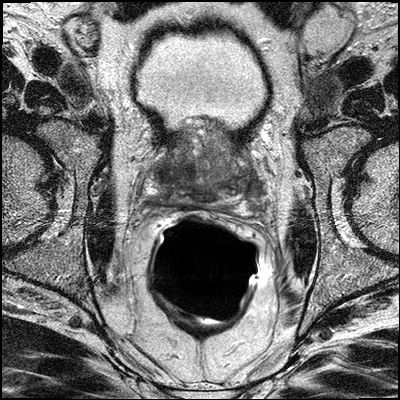
Multiparametric prostate MRI examination; 3 images, each a single mid-volume slice chosen by position (not for content). Treatment context recorded for this patient: Surgery.
Image 1: axial T2-weighted image, slice 19 of 36, 3 mm slice thickness.
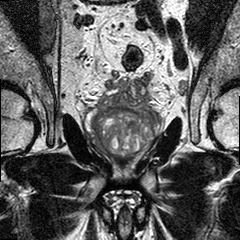
Image 2: T2-weighted coronal slice, series "T2W_TSE_COR", slice 14 of 26.
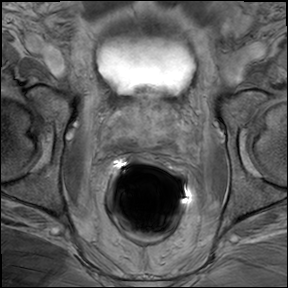
Image 3: DCE (dynamic gadolinium-enhanced) axial slice, slice 18 of 34, dynamic phase 5 of 8, 6 mm slice thickness.
Report of this MRI examination:
FINDINGS: The zonal anatomy is preserved. Due to BPH with prominent middle lobe of the prostate is enlarged measuring 5 x 4 x 5 cm resulting in an estimated volume of 52 cc There is diffuse signal alteration seen throughout the central gland consistent with BPH. There is a prominent middle lobe; There is also diffuse linear centrifugal signal alteration seen in the peripheral zones, due to chronic prostatitis, which might obscure small cancer foci. There are several sub 5 mm foci of suspicious enhancement seen in the left and right peripheral zones the prostate in all three levels (from base to apical third) . There is no suspicious enhancement of prostate capsule seen. There is no evidence of neural vascular bundle involvement. The folds of the seminal vesicles are thickened possible as consequences of longstanding BPH . Seminal vesicles infiltration therefore cannot be not entirely excluded, however no intraluminal masses seen in the seminal vesicles. Two rounded lymph node seen (12 x 8 and 9 x 11 mm respectively) along the iliac vessels on the right, just at the level and slightly above the right seminal vesicles, lateral to the urinary bladder. In addition several more small lymph nodes on both sides along the iliac vessels. IMPRESSION: Likely bilateral prostate tumor within enlarged prostate was marked BPH , middle lobe and chronic prostatitis. No evidence of extracapsular disease. The seminal vesicles show thickened walls which probably is a result of longstanding BPH. Beginning seminal vesicle infiltration could be obscured by this findings. Two right iliac > 10mm lymph nodes seen as described above, these are suspicious. PET CT recommended.

Prostatectomy specimen pathology (as recorded; the surgery followed this MRI):
Gross Description: A. "Left Lymph Node Pocket", B. "Right Lymph Node Pocket" and C. "Prostate and Seminal Vesicles". Specimen A consists of a 2.5x2x1 cm aggregate of fibrofatty tissue. The specimen is submitted entirely in two cassettes labeled A1 and A2. Specimen B consists of a 2.4x2x1 cm aggregate of fibrofatty tissue from which a single whole lymph node dissected. The entire specimen is submitted in cassettes as follows: B1 bisected single whole lymph node, B2 and B3 remaining fibroadipose tissue. Specimen C consists of a 57.1 gram, 4x3.5x3 cm radial prostatectomy specimen with attached right and left vas averaging 5 cm in length by 0.3 cm in diameter, right and left seminal vesicles averaging 3.8x1x0.5 cm. The specimen is inked as follows: right side black, left side blue. The specimen is transversely sectioned to reveal a vaguely nodular cut surface. Representative sections are submitted in cassettes as follows: C1 and C2 - radial section, proximal bladder base margin, C3 and C4 radial section, distal urethral margin, C5 thru C8 right anterior lobe, inferior to superior, C9 thru C12 right posterior lobe, inferior to superior, C13 thru C16 left posterior lobe, inferior to superior, C17 thru C20 left anterior lobe, inferior to superior, C21 right vas and right seminal vesicle, C22 left vas and left seminal vesicle.A: LEFT LYMPH NODE POCKET B: RIGHT LYMPH NODE POCKET C: PROSTATE AND SEMINAL VESICLES A. LEFT LYMPH NODE POCKET: FIVE (5) REACTIVE LYMPH NODES. NO TUMOR IDENTIFIED. B. RIGHT LYMPH NODE POCKET: TWO (2) REACTIVE LYMPH NODES. NO TUMOR IDENTIFIED. C. PROSTATE AND SEMINAL VESICLES: Prostate Size: 4x3.5X3cm Weight: 57.1g Histologic Type: Adenocarcinoma Histologic Grade: Primary Pattern Grade 3 Secondary Pattern Grade 4 Tertiary Pattern Grade 5 Total Gleason Score: 3+4=7/10 with focal tertiary Gleason pattern 5 (Less than1%) Approximate Proportion (percentage) of prostate involved by tumor: 40% Extraprostatic Extension: Not identified Seminal Vesicle Invasion: Not identified. Margins: Margins uninvolved by invasive carcinoma. Lymph-Vascular Invasion: Not identified. Perineural Invasion:Present. Pathologic Staging (pTNM) Primary Tumor (pT) pT2c:Bilateral disease Regional Lymph Nodes (pN) pNo: No regional lymph node metastasis. Specify: Number examined: 7 Number involved: 0. AJCC Pathologic Stage:(pT2c, pNo) High grade prostatic intraepithelial neoplasia (PIN.)Chronic inflammation